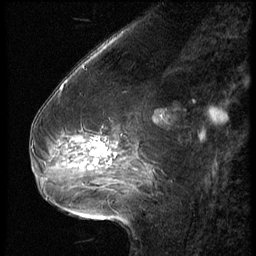
Breast MRI (dynamic contrast-enhanced), one sagittal slice. Position 22 of 62 along the scan axis. 3 images stored at this slice position (order not interpretable as contrast timing). 1.5 T. TE 4.2 ms, TR 9 ms. 2.5 mm slice thickness. 256 × 256 image matrix, field of view 180 × 180 mm. Patient: female, 54 years. From the clinical record (not read from this slice): setting: breast cancer imaged before/during neoadjuvant chemotherapy; receptor status: HR-positive, HER2-negative.
Annotated regions visible in this slice (semi-automatically segmented with operator editing):
- analysis volume of interest (the breast-tissue region the enhancement analysis was run in; not a lesion): box from (x=42, y=126) to (x=146, y=183) px
- tumour enhancement mask (voxels above the 140 % enhancement threshold inside the analysis volume of interest): (x=90, y=145)–(x=115, y=169)